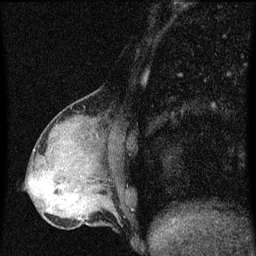
Breast MRI (dynamic contrast-enhanced), one sagittal slice; position 24 of 60 along the scan axis; dynamic contrast-enhanced series, image 2 of 3 at this slice position (ordered by acquisition); 1.5 T; TE 4.2 ms, TR 8 ms; 2 mm slice thickness; 256 × 256 image matrix, field of view 180 × 180 mm. Patient: female, 49 years.
Structures marked on this image (semi-automatic segmentation, software-assisted and operator-edited):
- analysis volume of interest (the breast-tissue region the enhancement analysis was run in; not a lesion): bounding box <43,190,88,219> (left, top, right, bottom; pixels)
- tumour enhancement mask (voxels above the 70 % enhancement threshold inside the analysis volume of interest): <67,198,72,205>